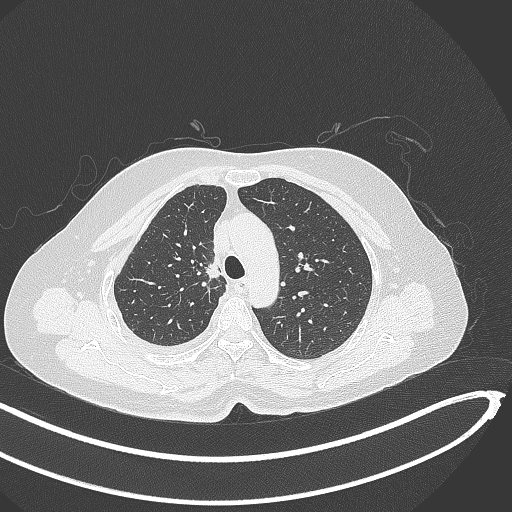
Chest CT, one axial slice; position 278 of 345 along the scan axis; lung window (W 1500 / L -600 HU); 1 mm slice thickness; 512 × 512 image matrix. Patient: female, 64 years. Case-level facts recorded for this patient, not image findings: clinical TNM (as recorded): T1b N0 M1.
Structures marked on this image (bounding box drawn by a radiologist):
- lung tumour (recorded histology: adenocarcinoma): bounding box [x1, y1, x2, y2] px = [203, 257, 225, 286]